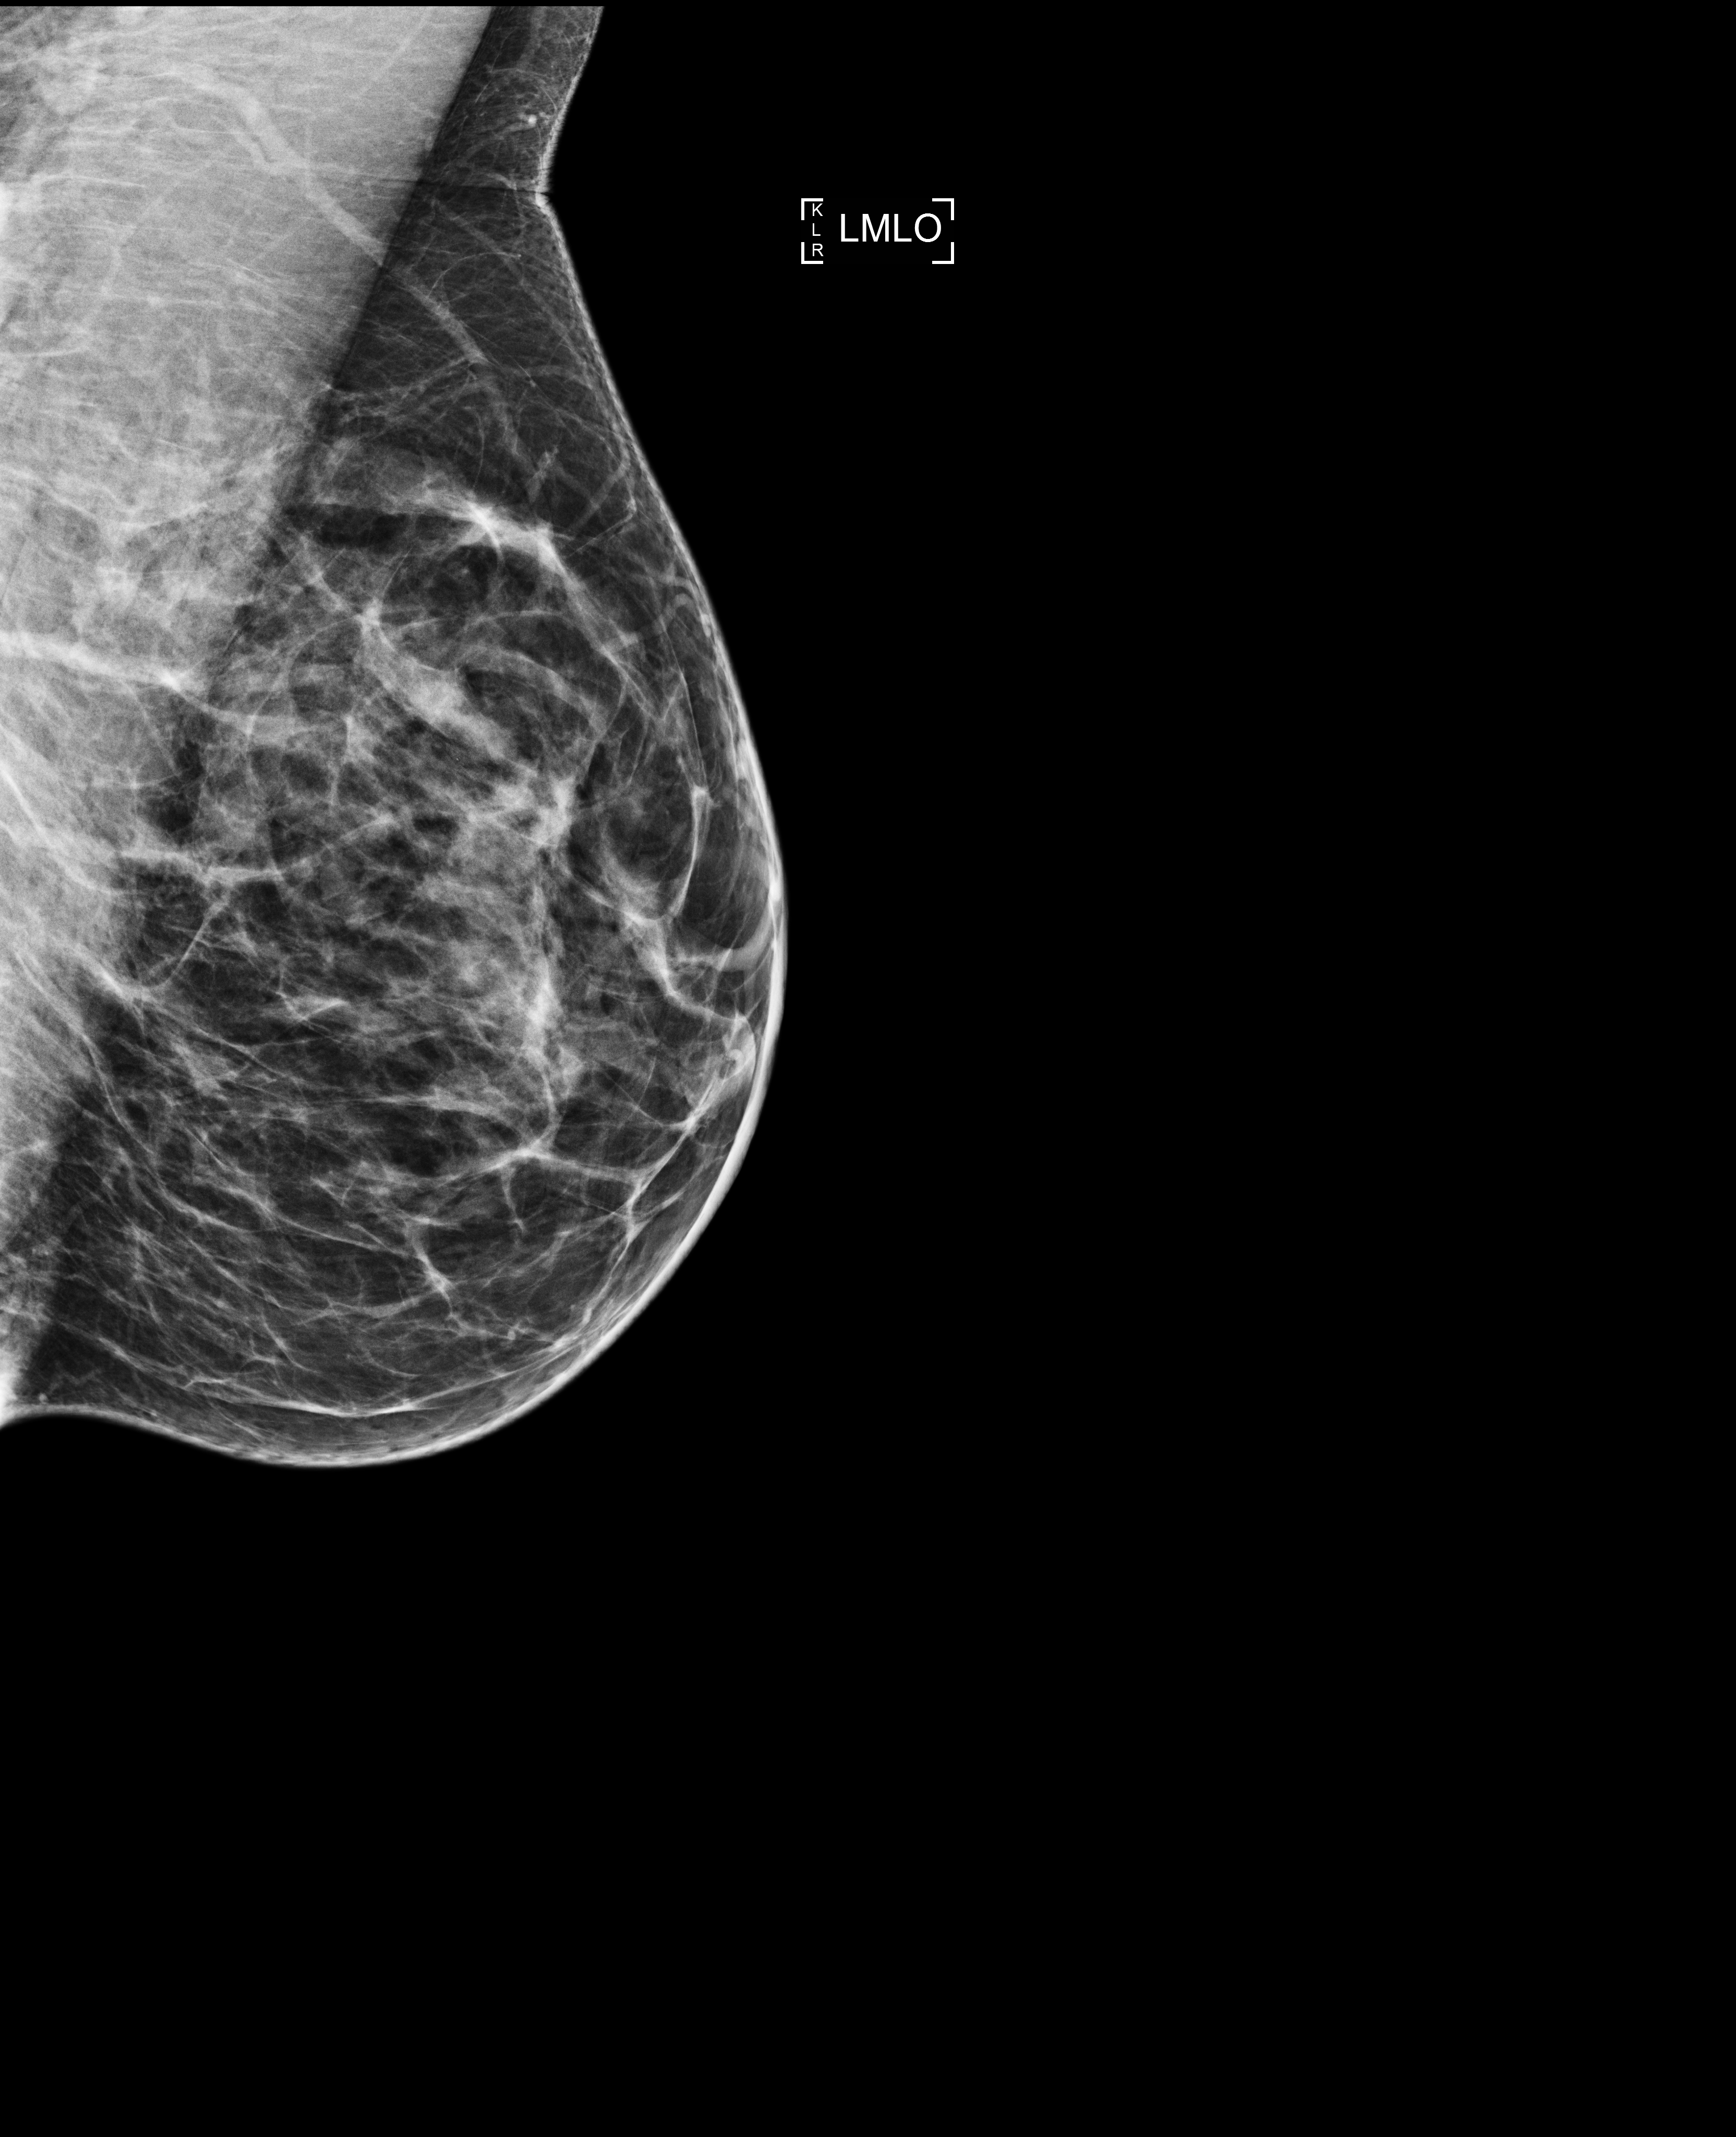
Screening examination. Female patient, age 41 years.
Image type: full-field digital mammogram. Breast: left. Projection: mediolateral oblique (MLO) view.